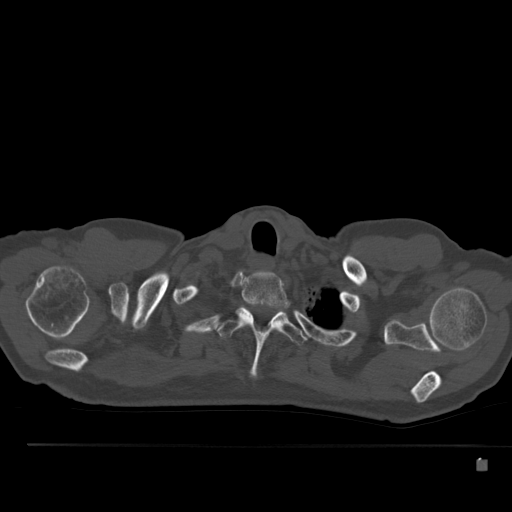
CT including the spine, one axial slice. Slice 419 of 517 in the series (ordered by position). Reconstruction kernel Br40s. Bone window (W 1800 / L 400 HU). 512 × 512 image matrix, field of view 408 × 408 mm. Male patient, age 70 years. From the clinical record (not read from this slice): primary cancer: renal.
Annotated regions visible in this slice (semi-automatic segmentation, software-assisted and operator-edited):
- T1 vertebra: box from (x=239, y=271) to (x=288, y=308) px
- T2 vertebra: (x=217, y=303)–(x=308, y=378)